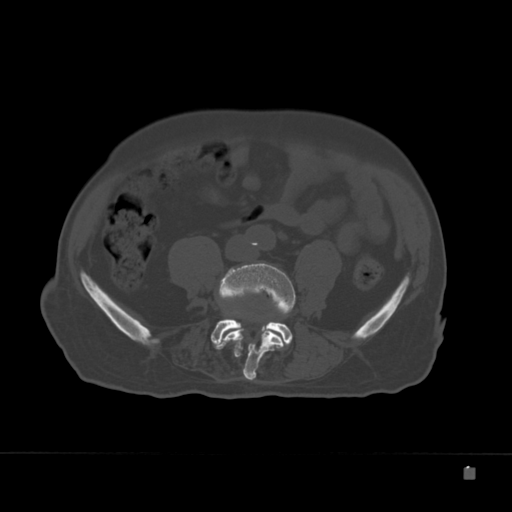
CT including the spine, one axial slice; 120 kVp; bone window (W 1800 / L 400 HU); 1.5 mm slice thickness; 512 × 512 image matrix, field of view 389 × 389 mm. Patient: male, 72 years. From the clinical record (not read from this slice): primary cancer: skeletal.
Structures marked on this image (semi-automatically segmented with operator editing):
- L4 vertebra: bounding box [x1, y1, x2, y2] px = [221, 263, 295, 381]
- L5 vertebra: [211, 319, 292, 349]